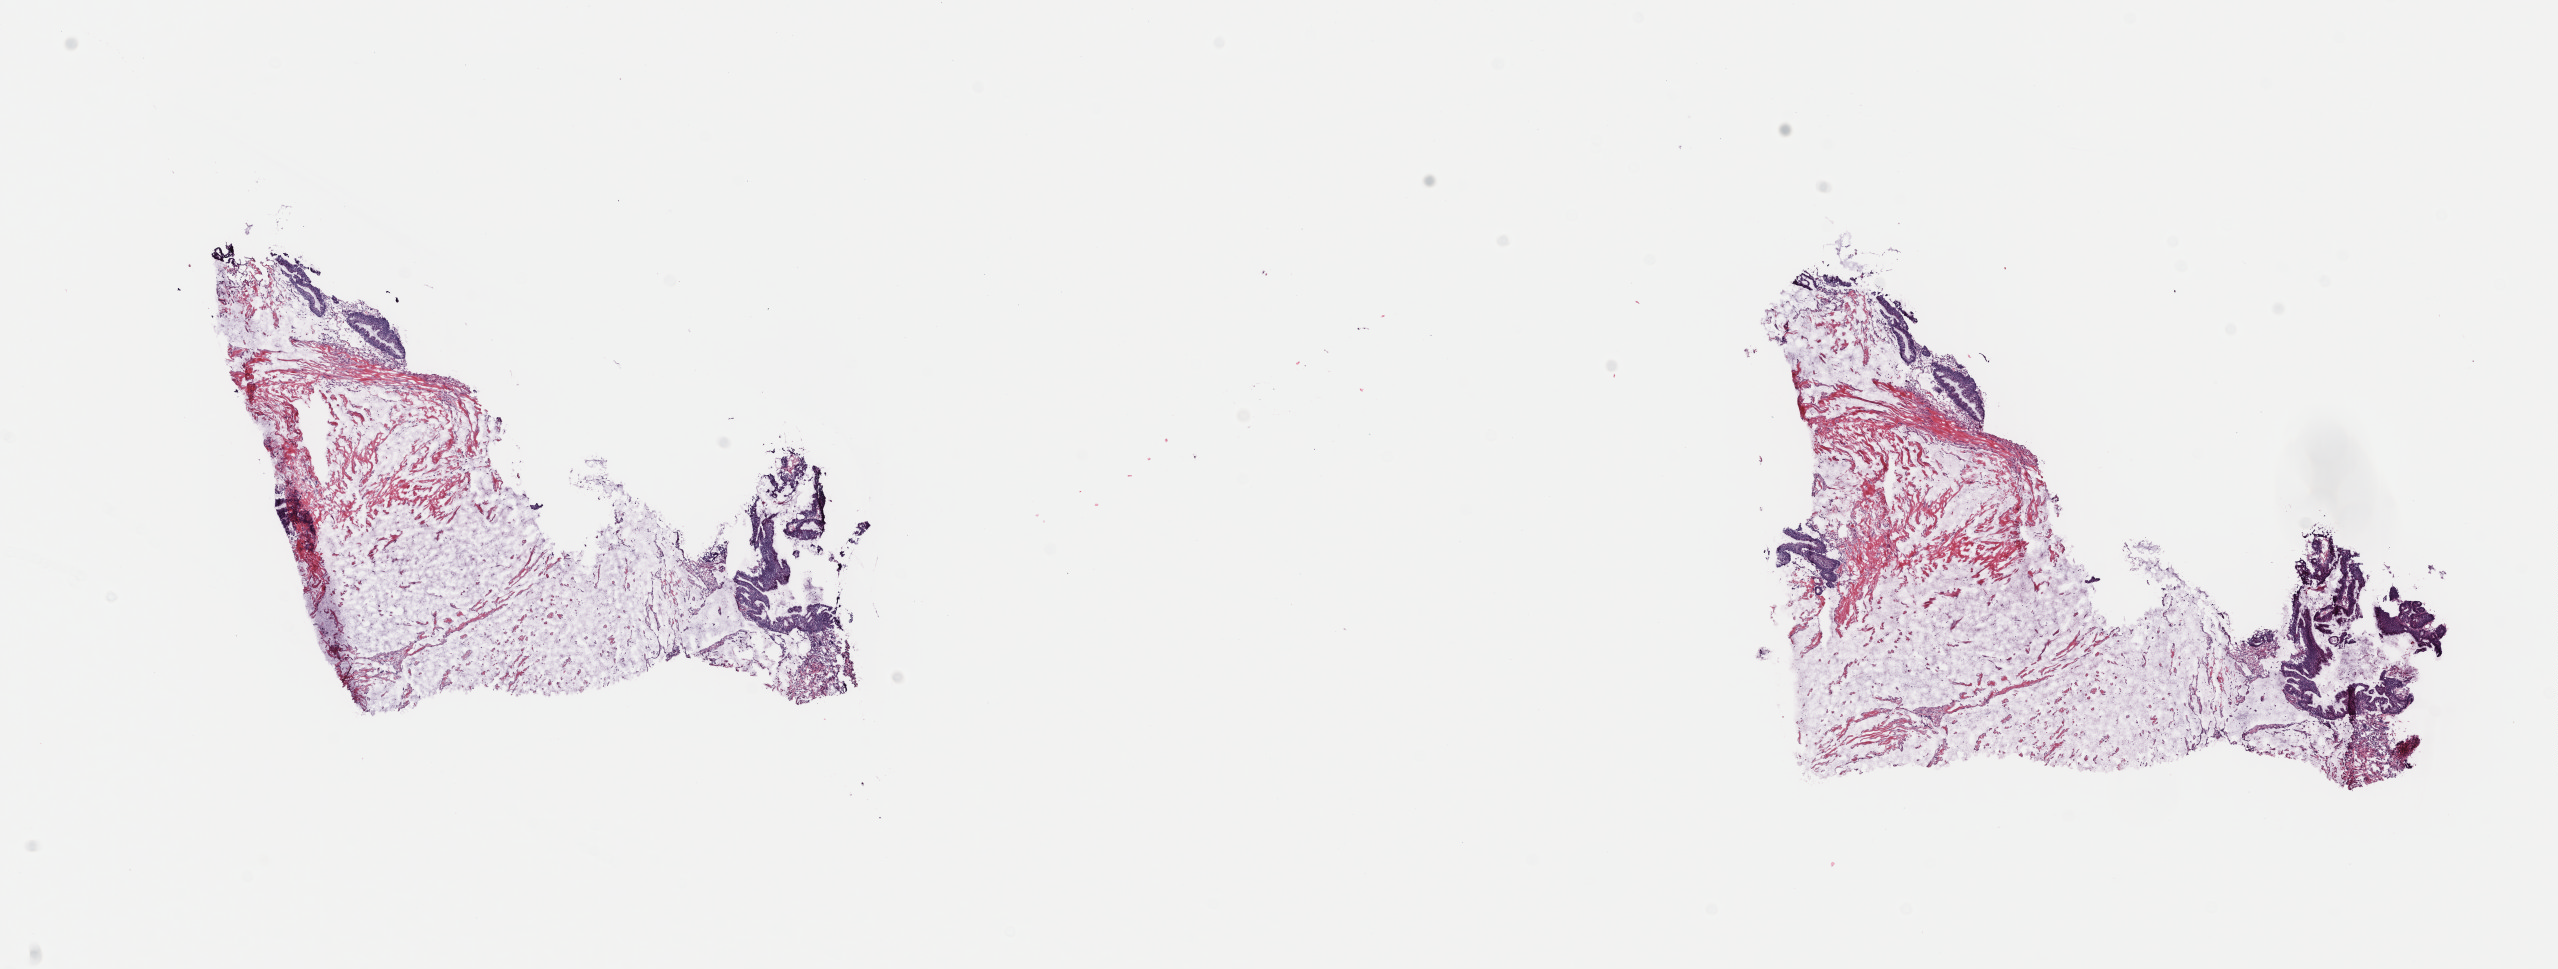
Whole-slide histology image, Hematoxylin and eosin (H&E) stained, a low-resolution overview of the entire scanned area, about 20.2 x 7.6 mm. Frozen section from the top of the tissue portion. Sample: primary tumour, colon. Female, age 66 years at initial diagnosis. Pathologist review of this section (percent, as recorded): tumour cells 65%, tumour nuclei 65%, normal cells 0%, stromal cells 33%, necrosis 2%. Infiltration values recorded for this section: lymphocyte infiltration 2%, monocyte infiltration 3%, neutrophil infiltration 2%.
TNM: T4b N1b M1b. AJCC pathologic stage: IVB (7th edition). Lymph nodes positive (case pathology): 3 of 19 examined. Histologic diagnosis: Mucinous adenocarcinoma (descending colon).